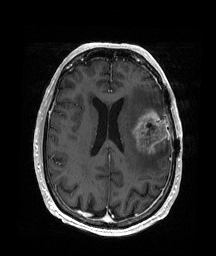
Brain MRI from a brain-tumour surgery series, one axial slice; position 76 of 176 along the scan axis; T1-weighted post-contrast; 1 mm slice thickness; 216 × 256 image matrix, field of view 219 × 260 mm. From the clinical record (not read from this slice): histopathology: Glioblastoma; WHO grade: 4; IDH mutation: no; tumour location: Left Frontal.
Annotated regions visible in this slice (outlined manually by an expert reader):
- tumour: bounding box [x1, y1, x2, y2] px = [132, 110, 169, 155]